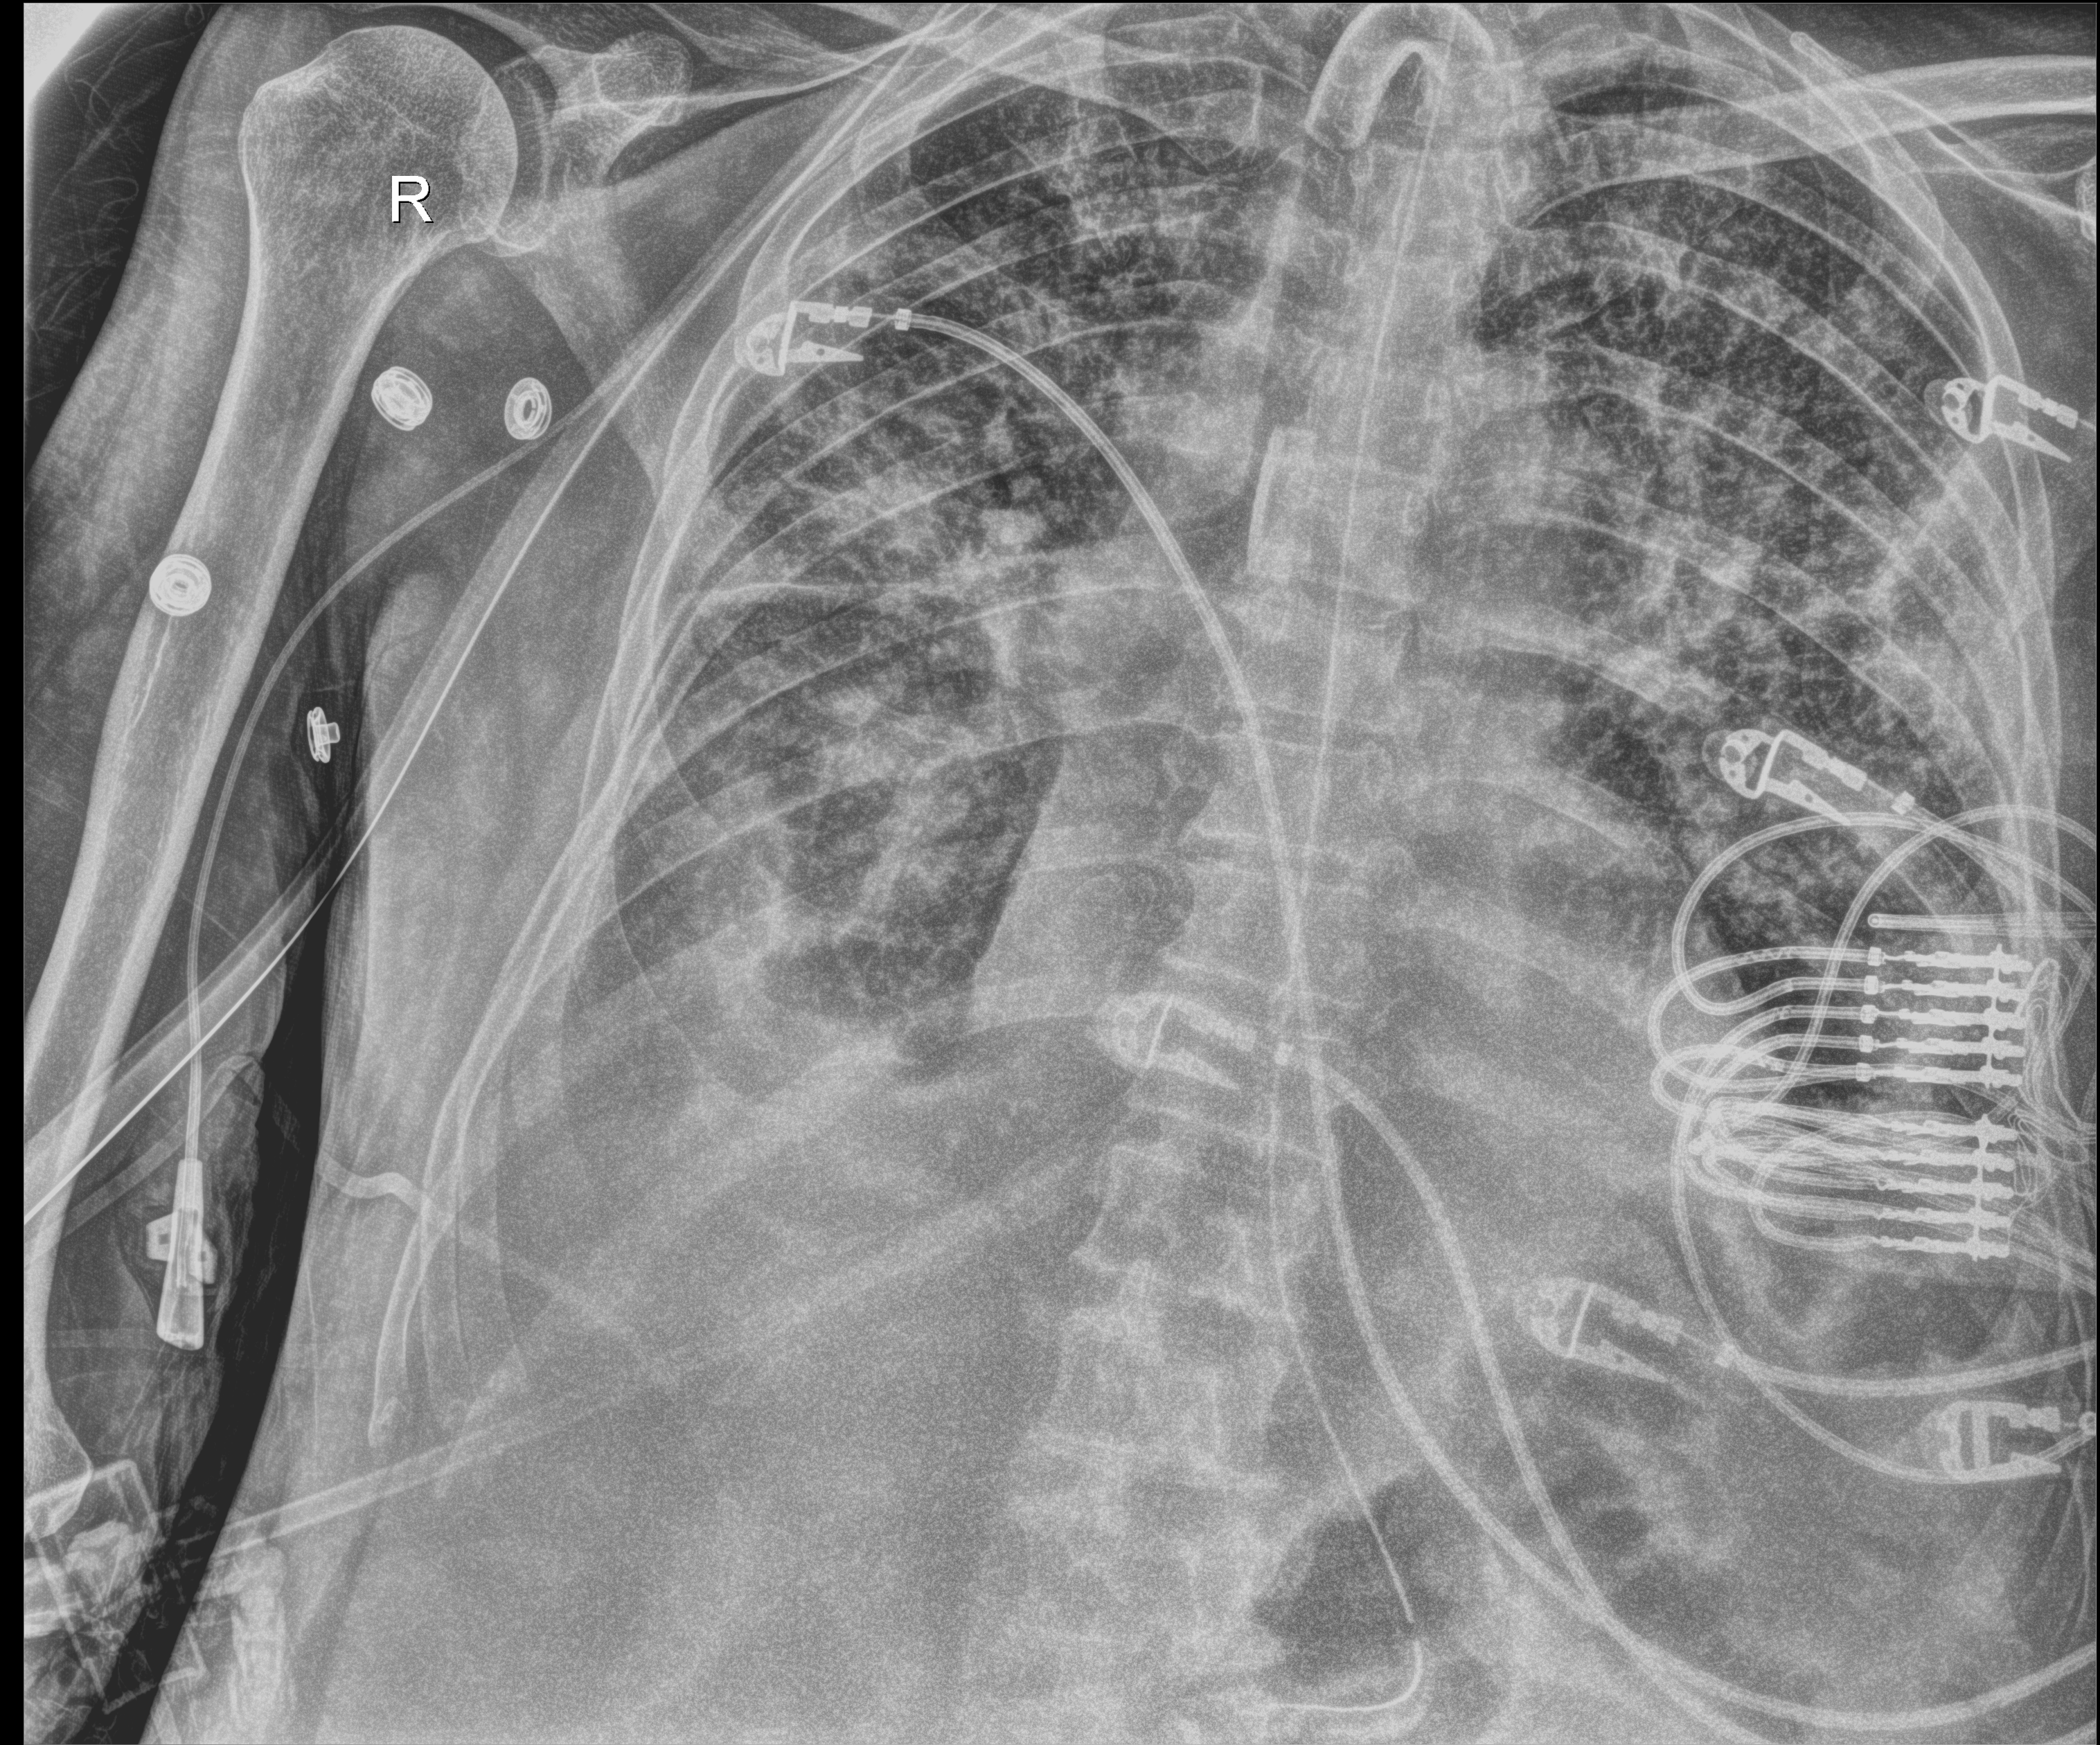
Portable chest radiograph, anteroposterior (AP) projection. Patient hospitalised with COVID-19; male, aged 75–90 years.
Admission-level facts for this patient (not findings on this image; timing relative to this image not recorded): mechanically ventilated during this hospital stay: yes; chronic kidney disease (admission record): no.